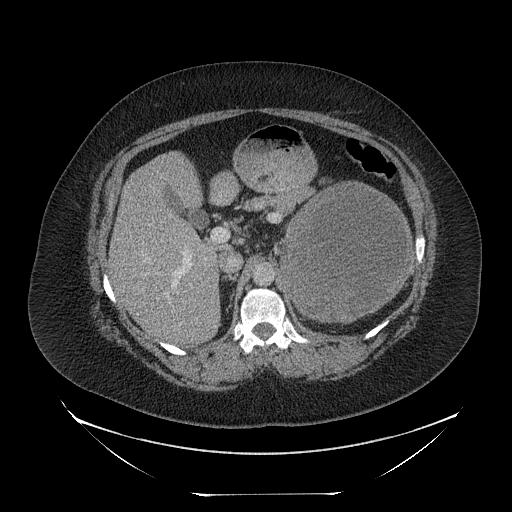
Contrast-enhanced abdominal CT, one axial slice. Position 148 of 205 along the scan axis. 120 kVp. Intravenous contrast given. Soft-tissue window (W 400 / L 40 HU). 2.5 mm slice thickness. 512 × 512 image matrix. Female patient, age 53 years. Case-level facts recorded for this patient, not image findings: diagnosis: adrenocortical carcinoma; tumour side: left adrenal; tumour size at pathology: 17 cm.
Structures marked on this image (semi-automatic segmentation, software-assisted and operator-edited):
- mass: bounding box [x1, y1, x2, y2] px = [283, 184, 412, 320]